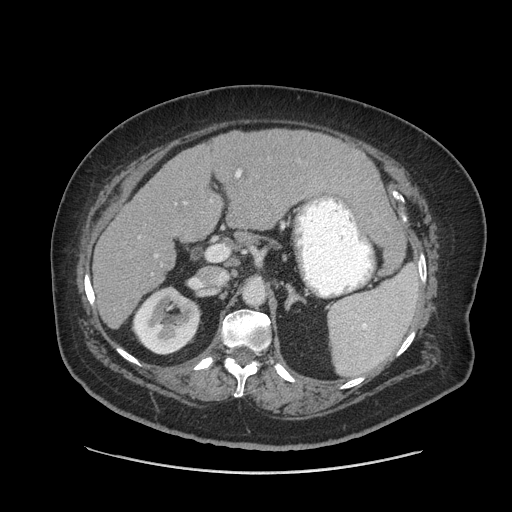
Contrast-enhanced abdominal CT (liver protocol), one axial slice. Position 44 of 91 along the scan axis. 140 kVp. Soft-tissue window (W 400 / L 40 HU). 2.5 mm slice thickness. 512 × 512 image matrix, field of view 420 × 420 mm. Case-level facts recorded for this patient, not image findings: diagnosis: hepatocellular carcinoma (patient treated with transarterial chemoembolisation; whether this scan precedes or follows treatment is not stated here); TNM stage (as recorded): Stage-I; Child-Pugh class: A; tumour differentiation: well differentiated; tumour nodularity: uninodular.
Structures marked on this image (semi-automatically segmented with operator editing):
- liver parenchyma outside the tumour (the mass and vessels are separate outlines, so this box may not span the whole liver): bounding box [x1, y1, x2, y2] px = [92, 129, 386, 328]
- liver vessels: [156, 170, 242, 257]